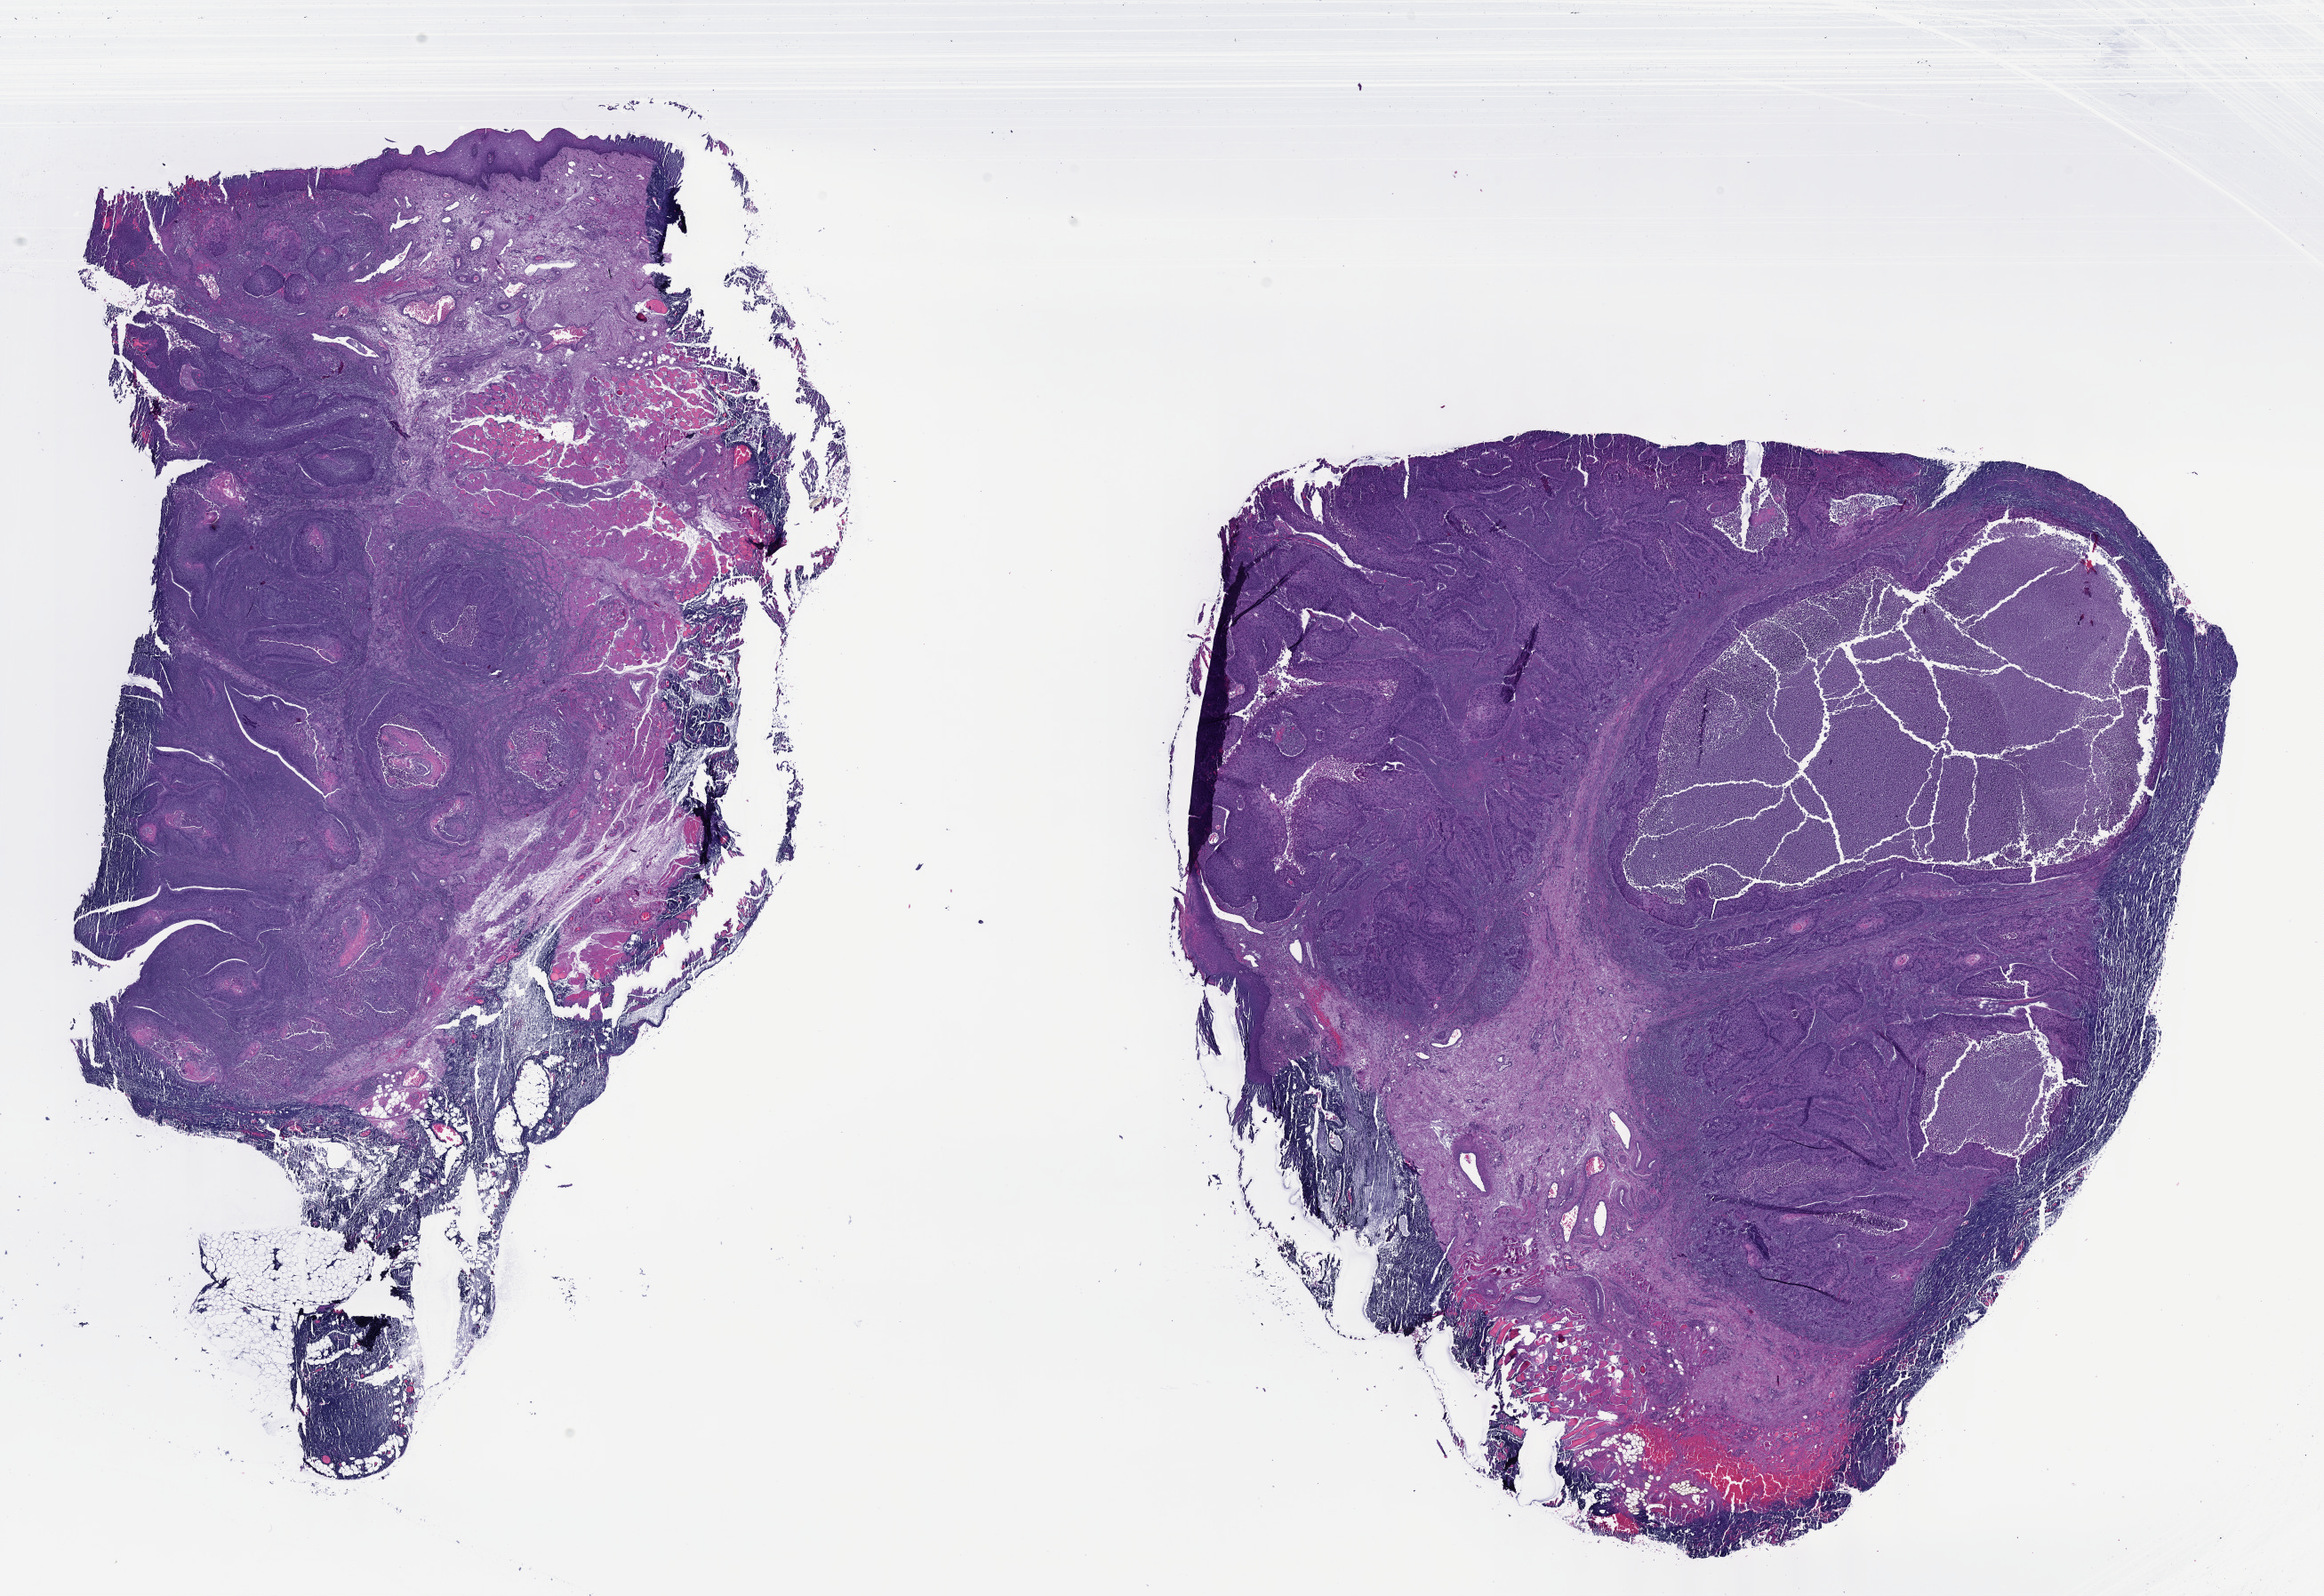
Whole-slide histology image, Hematoxylin and eosin (H&E) stained — whole scanned area (about 21.1 x 14.5 mm) shown as a low-resolution overview, FFPE section, primary tumour sample from the head and neck. Patient: male, age at initial diagnosis 60 years. Histologic grade: G2 (moderately differentiated).
AJCC pathologic stage: IVA. Diagnosis: Squamous cell carcinoma, NOS (larynx, NOS). TNM: T4a N2b.